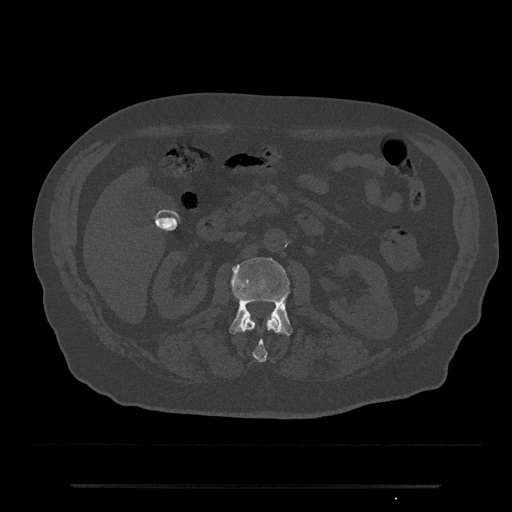
CT including the spine, one axial slice; position 495 of 797 along the scan axis; 120 kVp; bone window (W 1800 / L 400 HU); 0.5 mm slice thickness; 512 × 512 image matrix, field of view 434 × 434 mm. Patient: male, 80 years. Case-level facts recorded for this patient, not image findings: primary cancer: prostate; vertebrae with lytic lesions (as recorded): L1, T11.
Structures marked on this image (semi-automatic segmentation, software-assisted and operator-edited):
- L1 vertebra: bounding box [x1, y1, x2, y2] px = [242, 317, 281, 362]
- L2 vertebra: [229, 258, 293, 335]